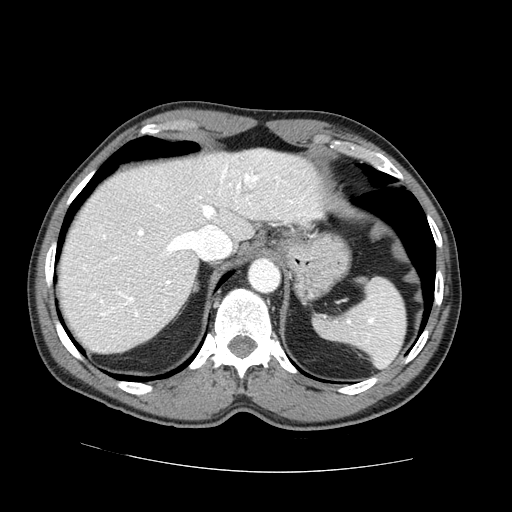
Contrast-enhanced abdominal CT (liver protocol), one axial slice; position 56 of 73 along the scan axis; 100 kVp; one of 2 acquisitions stored at this slice position; soft-tissue window (W 400 / L 40 HU); 512 × 512 image matrix. From the clinical record (not read from this slice): diagnosis: hepatocellular carcinoma (patient treated with transarterial chemoembolisation; whether this scan precedes or follows treatment is not stated here); TNM stage (as recorded): Stage-IVA; Child-Pugh class: A.
Structures marked on this image (semi-automatic segmentation, software-assisted and operator-edited):
- abdominal aorta: bounding box <250,259,280,292> (left, top, right, bottom; pixels)
- liver parenchyma outside the tumour (the mass and vessels are separate outlines, so this box may not span the whole liver): <58,148,322,352>
- liver vessels: <84,153,293,316>